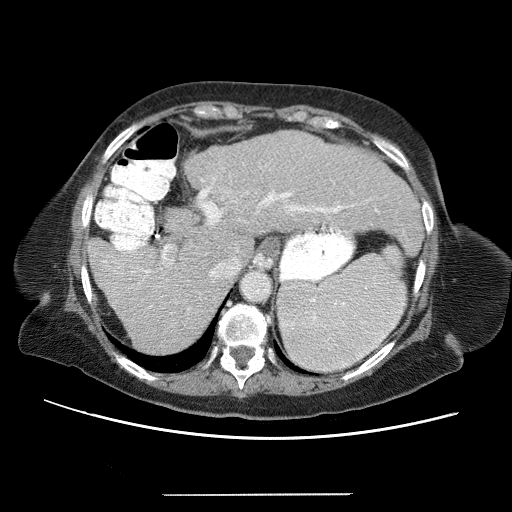
Contrast-enhanced abdominal CT (liver protocol), one axial slice; slice 44 of 65 in the series (ordered by position); 120 kVp; soft-tissue window (W 400 / L 40 HU); 2.5 mm slice thickness; 512 × 512 image matrix, field of view 380 × 380 mm. From the clinical record (not read from this slice): diagnosis: hepatocellular carcinoma (patient treated with transarterial chemoembolisation; whether this scan precedes or follows treatment is not stated here); TNM stage (as recorded): Stage-IIIB; Child-Pugh class: A.
Structures marked on this image (semi-automatically segmented with operator editing):
- liver parenchyma outside the tumour (the mass and vessels are separate outlines, so this box may not span the whole liver): bounding box <89,132,420,352> (left, top, right, bottom; pixels)
- mass: <162,243,176,263>
- liver vessels: <99,157,418,327>